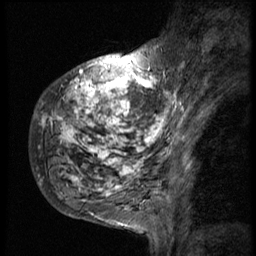
Breast MRI (dynamic contrast-enhanced), one sagittal slice; position 15 of 58 along the scan axis; 3 images stored at this slice position (order not interpretable as contrast timing); 1.5 T; TE 4.2 ms, TR 9 ms; 256 × 256 image matrix. Female patient, age 50 years. From the clinical record (not read from this slice): setting: breast cancer imaged before/during neoadjuvant chemotherapy; receptor status: triple-negative.
Outlined on this slice (semi-automatic segmentation, software-assisted and operator-edited):
- analysis volume of interest (the breast-tissue region the enhancement analysis was run in; not a lesion): bounding box (x1, y1, x2, y2) in pixels: (31, 48, 186, 214)
- tumour enhancement mask (voxels above the 140 % enhancement threshold inside the analysis volume of interest): (37, 50, 186, 214)